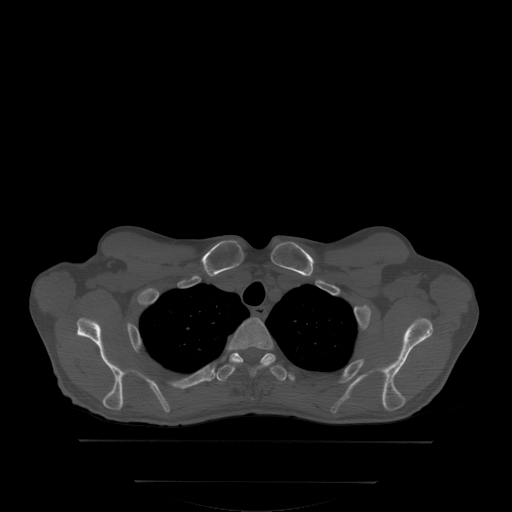
CT including the spine, one axial slice; position 274 of 350 along the scan axis; bone window (W 1800 / L 400 HU); 2.5 mm slice thickness; 512 × 512 image matrix, field of view 500 × 500 mm. Male patient, age 58 years. From the clinical record (not read from this slice): primary cancer: prostate; vertebrae with lytic lesions (as recorded): L1.
Structures marked on this image (semi-automatic segmentation, software-assisted and operator-edited):
- T2 vertebra: bounding box (x1, y1, x2, y2) in pixels: (228, 317, 276, 376)
- T3 vertebra: (216, 352, 287, 381)